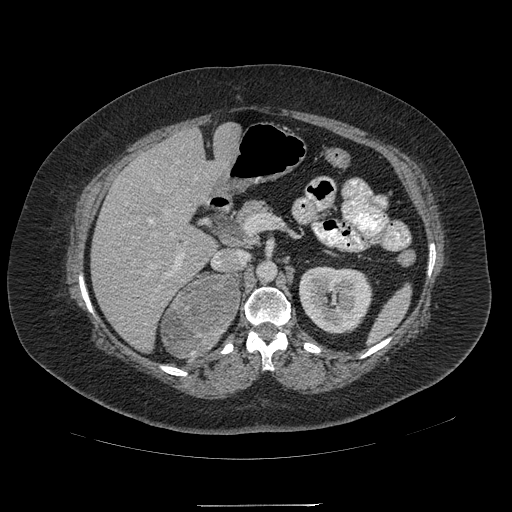
Contrast-enhanced abdominal CT, one axial slice; position 121 of 217 along the scan axis; reconstruction kernel STANDARD; 120 kVp; intravenous contrast given; soft-tissue window (W 400 / L 40 HU); 1.25 mm slice thickness; 512 × 512 image matrix, field of view 453 × 453 mm. Female patient, age 55 years. Case-level facts recorded for this patient, not image findings: diagnosis: adrenocortical carcinoma; tumour side: right adrenal; tumour size at pathology: 11 cm; Ki-67 index: 20 %; stage (as recorded): 2.
Outlined on this slice (semi-automatically segmented with operator editing):
- mass: bounding box <162,275,238,357> (left, top, right, bottom; pixels)